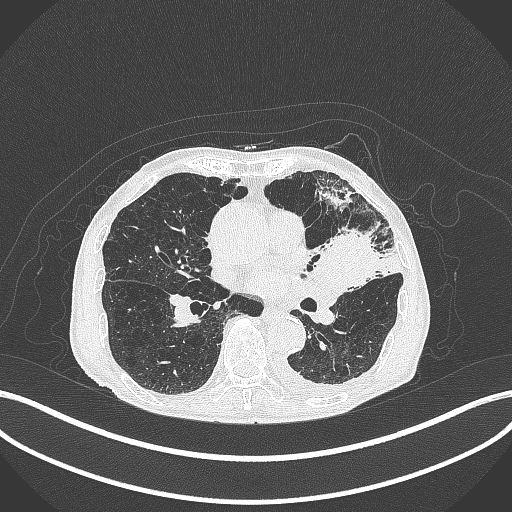
Chest CT, one axial slice. Position 189 of 385 along the scan axis. Reconstruction kernel B70f. 120 kVp. Lung window (W 1500 / L -600 HU). 1 mm slice thickness. 512 × 512 image matrix, field of view 400 × 400 mm. Male patient, age 90 years or older. Case-level facts recorded for this patient, not image findings: clinical TNM (as recorded): T2b N1 M0.
Outlined on this slice (rectangle marked by the reading radiologist):
- lung tumour (recorded histology: squamous cell carcinoma): bounding box [x1, y1, x2, y2] px = [305, 229, 381, 295]